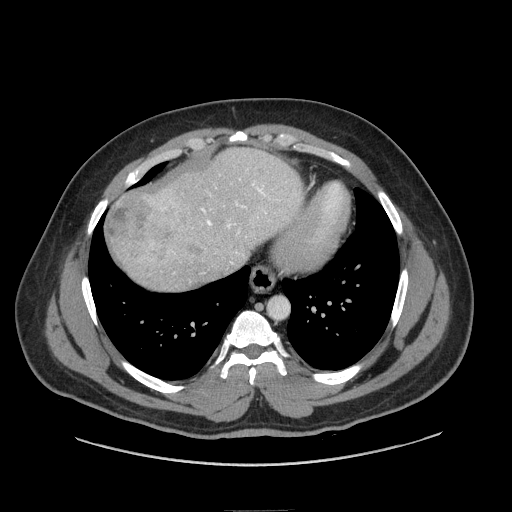
Contrast-enhanced abdominal CT (liver protocol), one axial slice; slice 70 of 87 in the series (ordered by position); reconstruction kernel STANDARD; 140 kVp; soft-tissue window (W 400 / L 40 HU); 512 × 512 image matrix. Case-level facts recorded for this patient, not image findings: diagnosis: hepatocellular carcinoma (patient treated with transarterial chemoembolisation; whether this scan precedes or follows treatment is not stated here); TNM stage (as recorded): Stage-II; Child-Pugh class: A; tumour differentiation: moderately differentiated; tumour nodularity: uninodular.
Structures marked on this image (semi-automatic segmentation, software-assisted and operator-edited):
- abdominal aorta: bounding box (x1, y1, x2, y2) in pixels: (268, 297, 288, 318)
- liver parenchyma outside the tumour (the mass and vessels are separate outlines, so this box may not span the whole liver): (108, 148, 302, 290)
- mass: (106, 191, 188, 264)
- liver vessels: (161, 187, 265, 233)